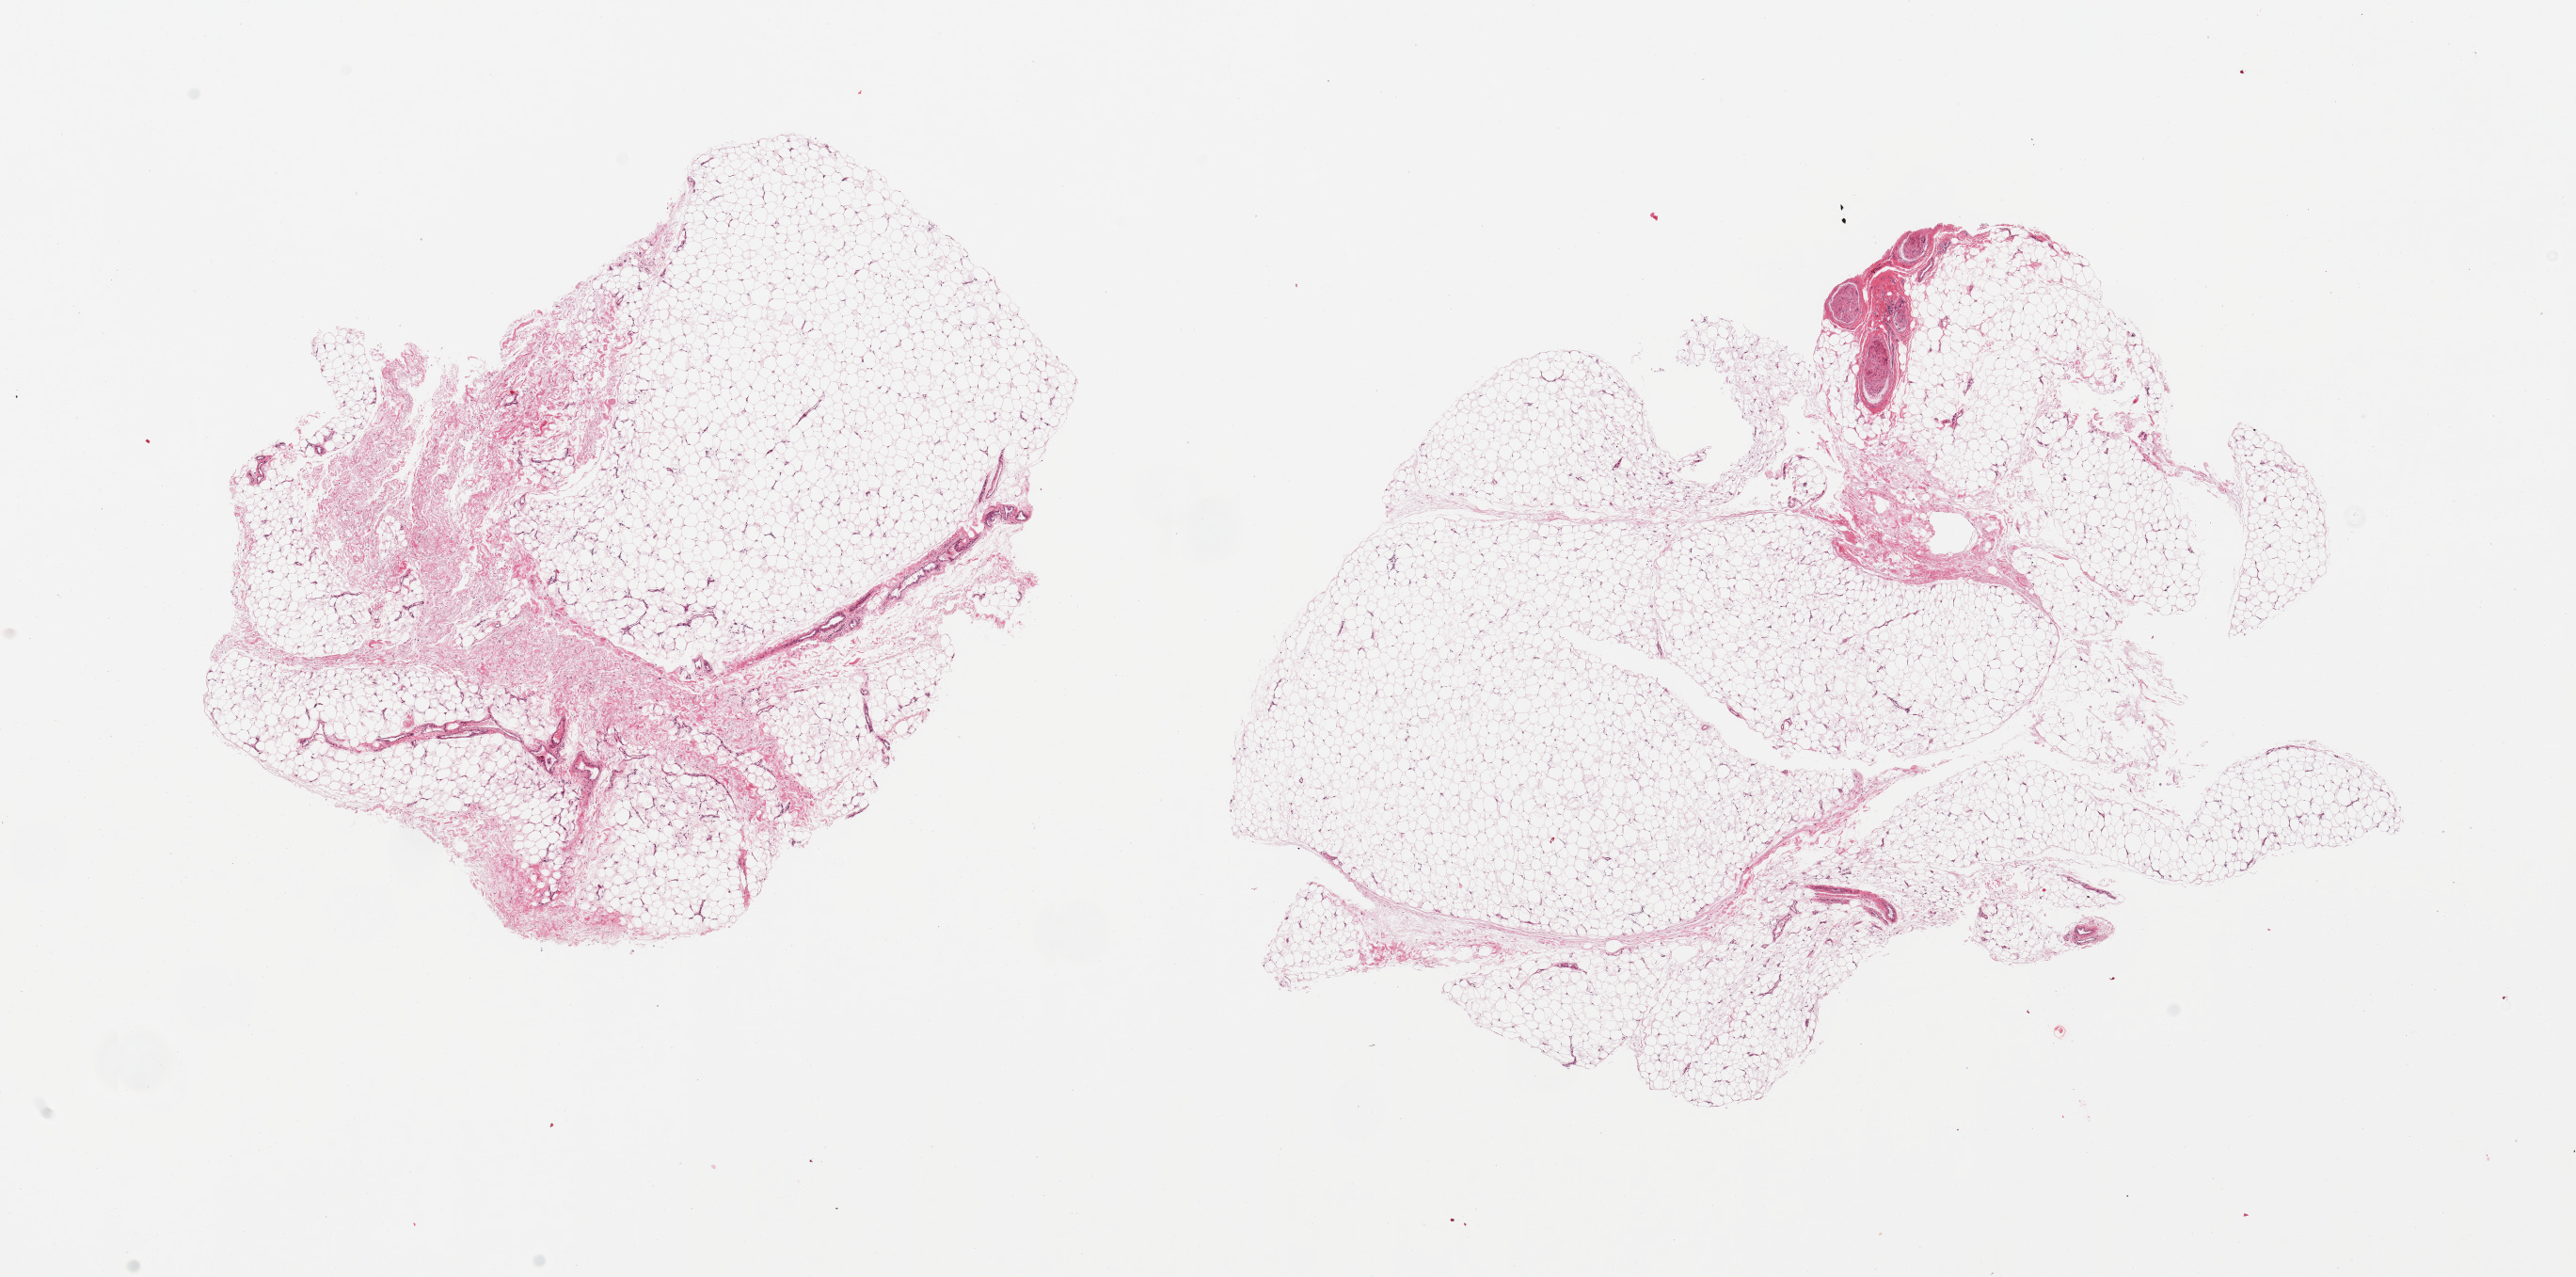
Digitized hematoxylin and eosin (H&E)-stained section, brightfield — a low-resolution overview of the entire scanned area, about 21.7 x 10.7 mm, PAXgene-fixed paraffin-embedded (PFPE) section, target tissue: adipose tissue, tissue donor sample. Male donor.
Review note (as recorded): 2 pieces; 1 mm sq nerve in 1 piece; 20% fibrous tissue in other piece.